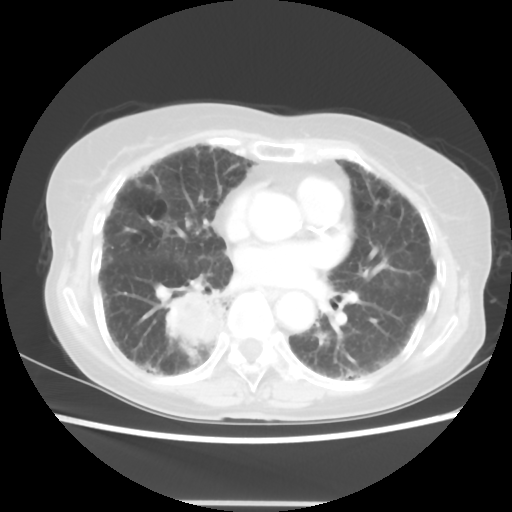
Chest CT, one axial slice; position 25 of 52 along the scan axis; 120 kVp; lung window (W 1500 / L -600 HU); 512 × 512 image matrix, field of view 325 × 325 mm. Patient: female, 71 years. From the clinical record (not read from this slice): clinical TNM (as recorded): T3 N0 M0.
Structures marked on this image (rectangle marked by the reading radiologist):
- lung tumour (recorded histology: squamous cell carcinoma): box from (x=157, y=283) to (x=228, y=355) px